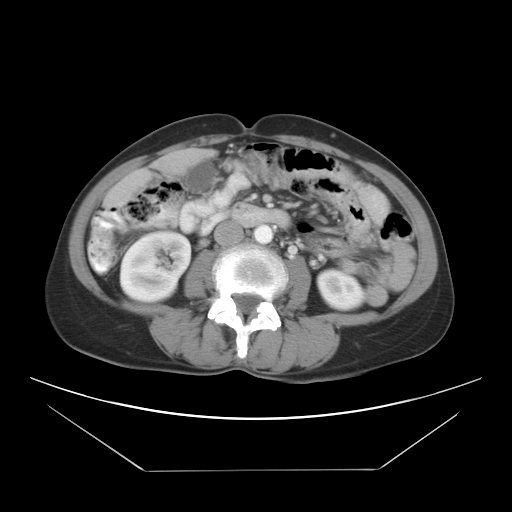
Contrast-enhanced abdominal CT, one axial slice. Slice 6 of 30 in the series (ordered by position). Intravenous contrast given. Soft-tissue window (W 400 / L 40 HU). 7.5 mm slice thickness. 512 × 512 image matrix. Female patient, age 54 years. Case-level facts recorded for this patient, not image findings: diagnosis: colorectal cancer liver metastases, imaged before liver resection.
Annotated regions visible in this slice (manually delineated by an expert):
- liver: box from (x=113, y=151) to (x=201, y=201) px
- planned liver remnant (the part of the liver to remain after resection): (x=127, y=150)–(x=202, y=186)